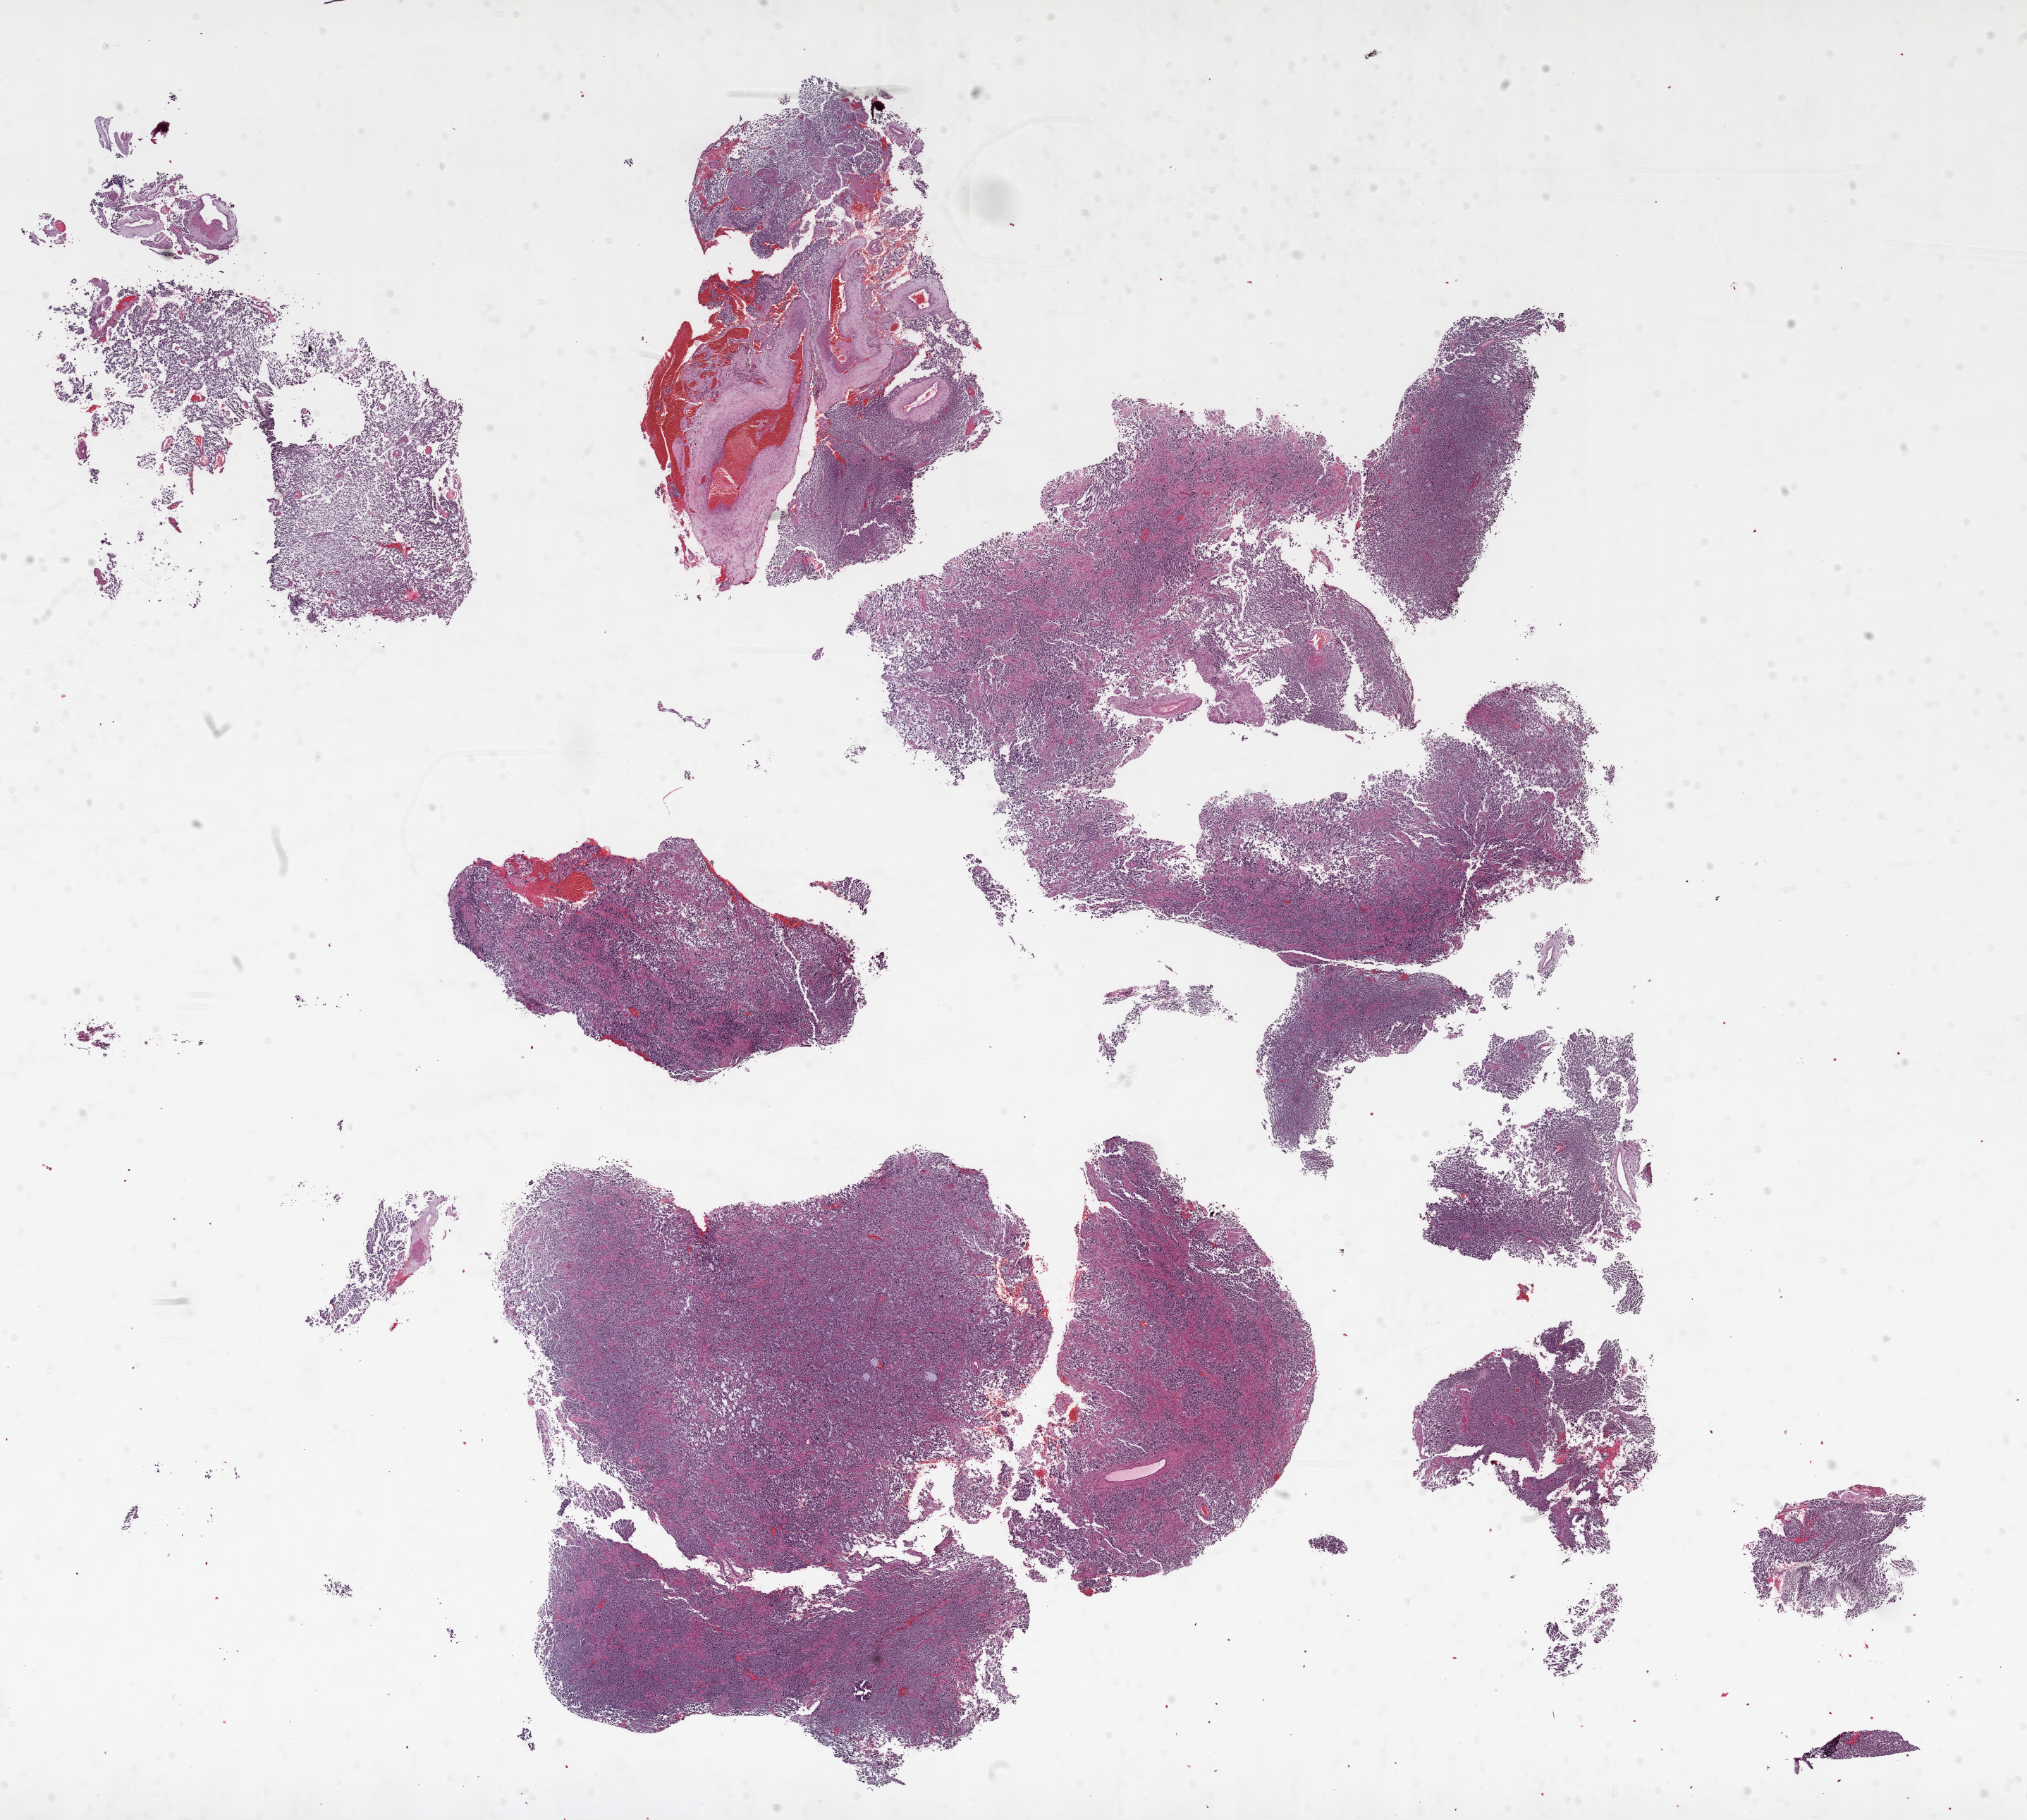
Hematoxylin and eosin (H&E) stained whole-slide image, whole scanned area (about 23.1 x 20.7 mm) shown as a low-resolution overview. FFPE section. Brain, primary tumour sample. Male, age 31 years at initial diagnosis.
• histologic diagnosis: Glioblastoma